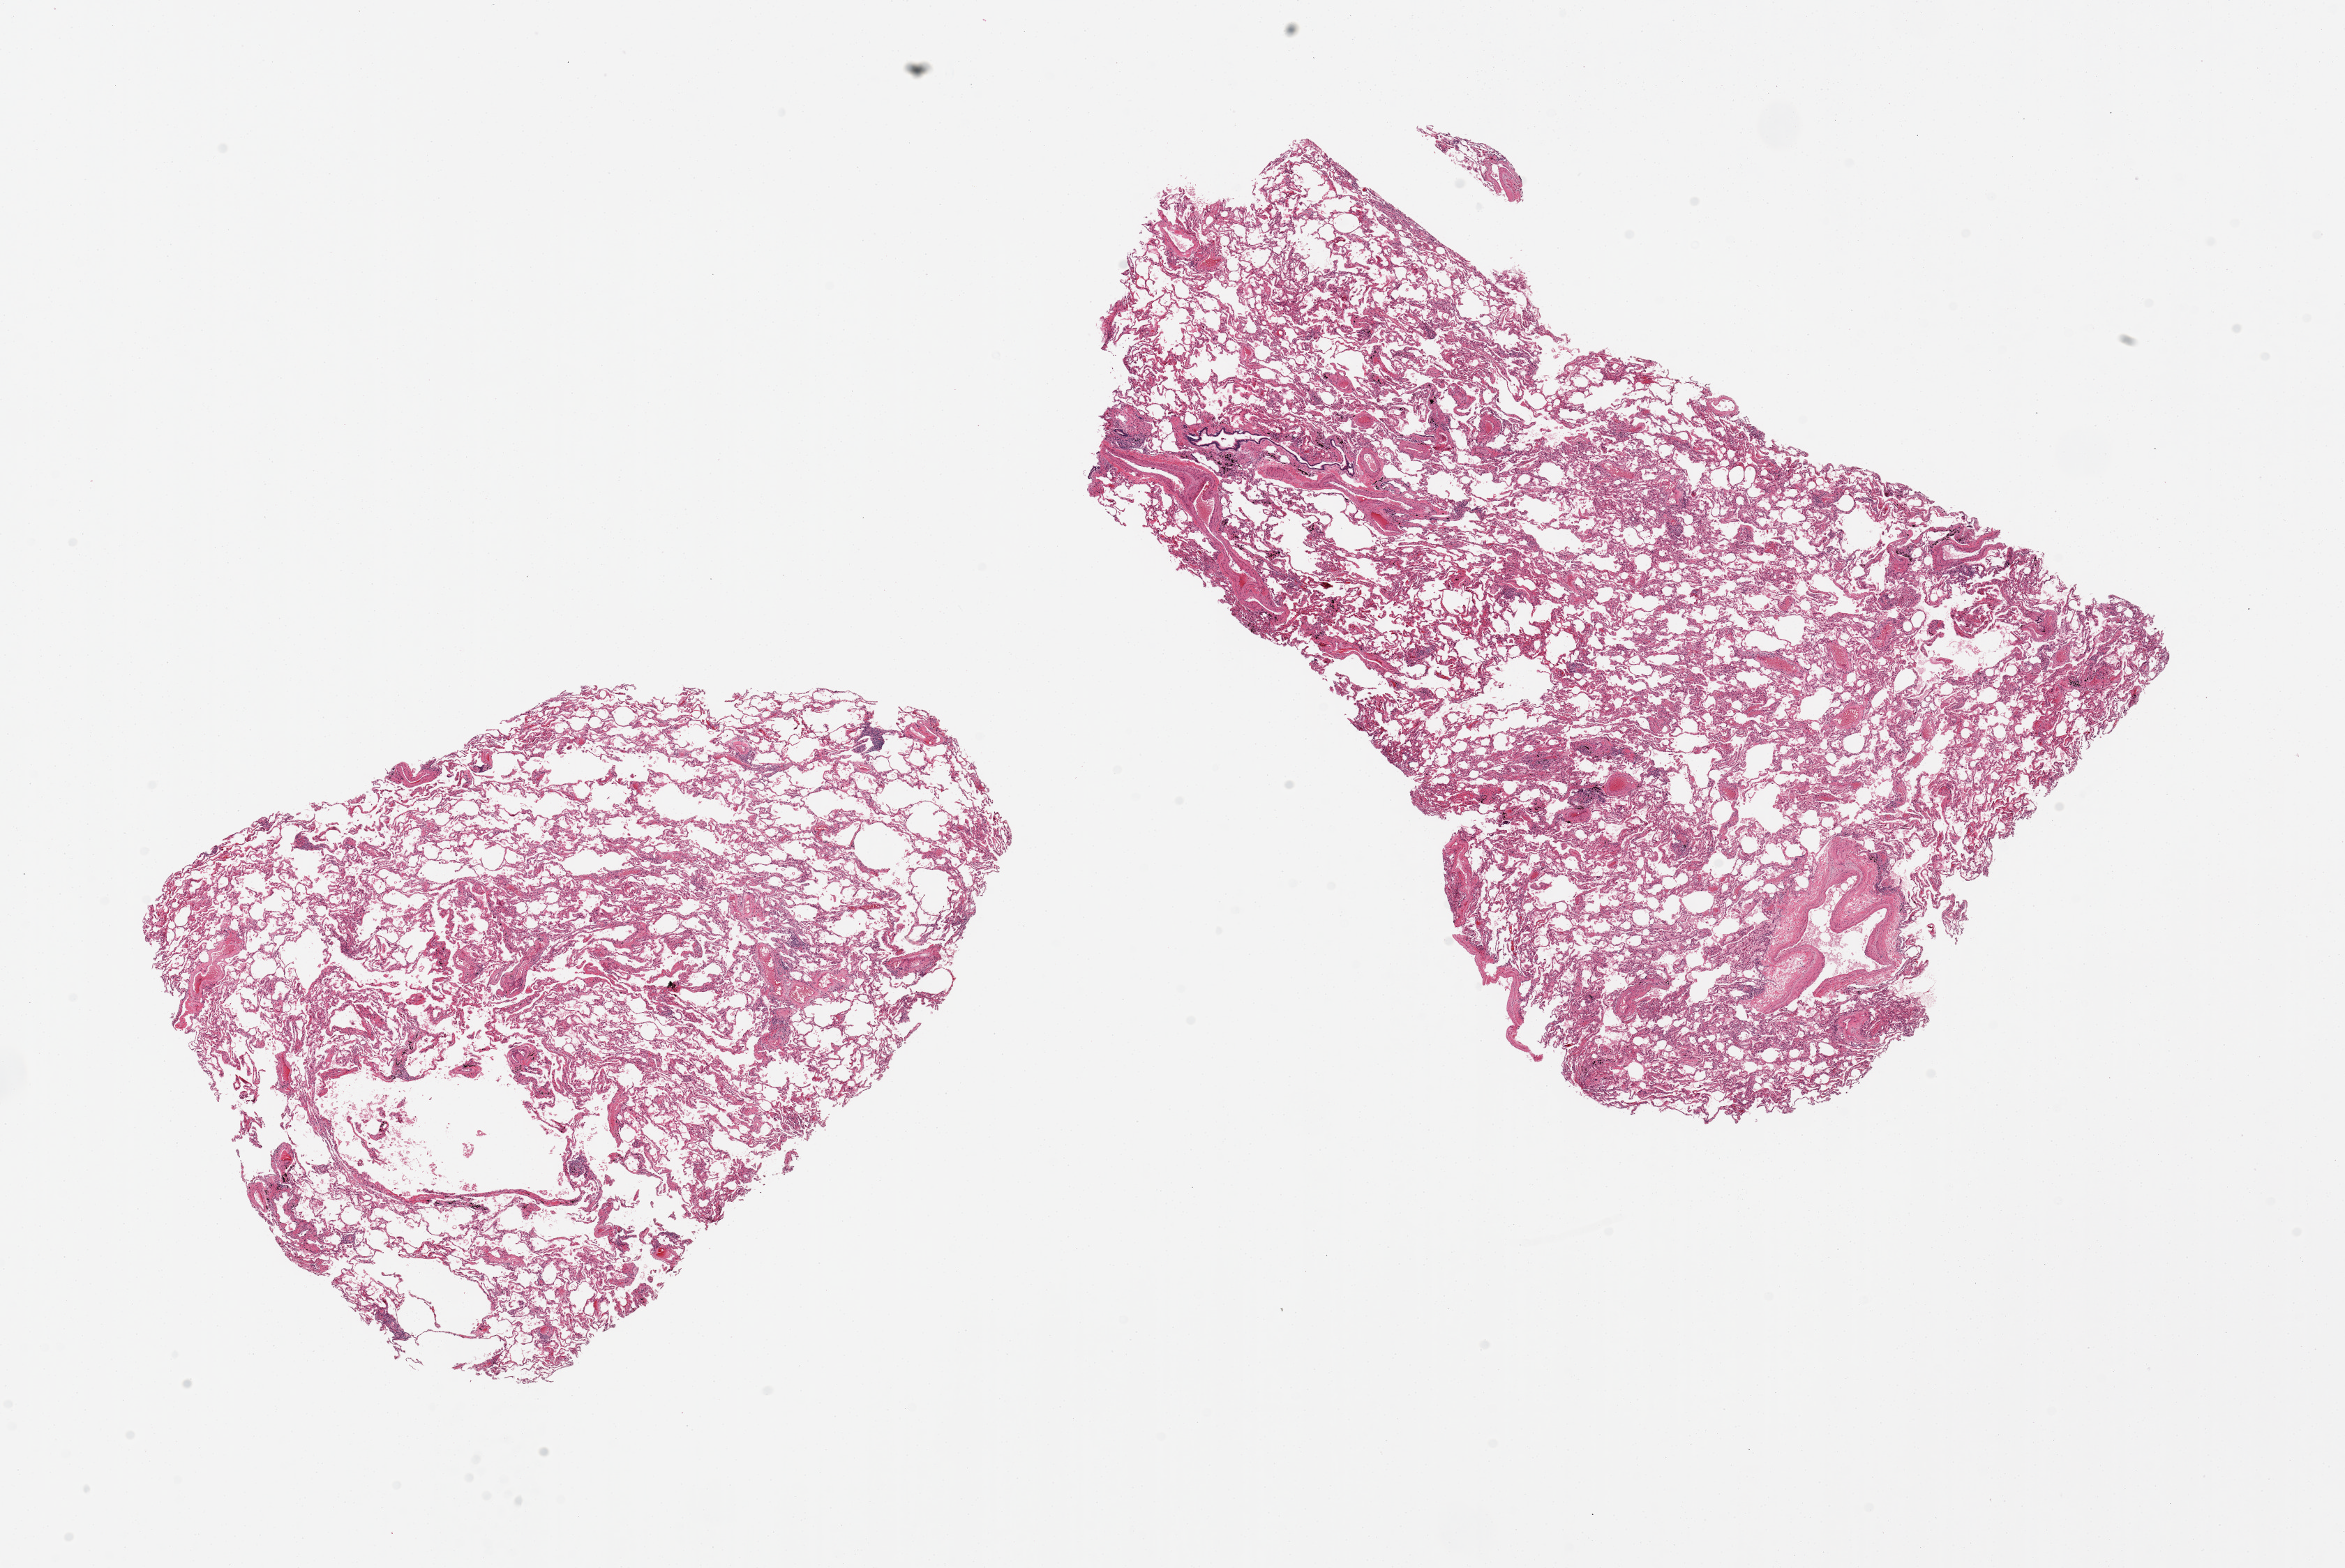
Whole-slide image, hematoxylin and eosin (H&E) stain, brightfield, low-resolution overview of the scanned area, about 26.6 x 17.8 mm (acquisition: 20x scan), PAXgene-fixed paraffin-embedded (PFPE) section, target tissue: lung, tissue donor sample. Donor: female.
- review note (as recorded): 2 pieces, 10x7 & 12.5x8.5mm; emphysematous changes, carbon particle deposition